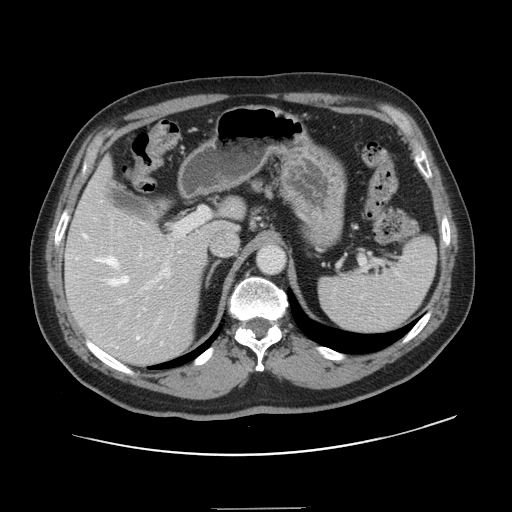
Contrast-enhanced abdominal CT, one axial slice. Intravenous contrast given. Soft-tissue window (W 400 / L 40 HU). 2.5 mm slice thickness. 512 × 512 image matrix. Male patient, age 62 years. Case-level facts recorded for this patient, not image findings: diagnosis: colorectal cancer liver metastases, imaged before liver resection; multiple liver metastases: yes; largest metastasis: 2.7 cm; disease in both lobes: no.
Outlined on this slice (expert manual segmentation):
- hepatic veins: bounding box <83,234,162,348> (left, top, right, bottom; pixels)
- liver: <66,165,242,363>
- planned liver remnant (the part of the liver to remain after resection): <69,164,242,249>
- portal vein (with intrahepatic branches): <76,208,210,303>